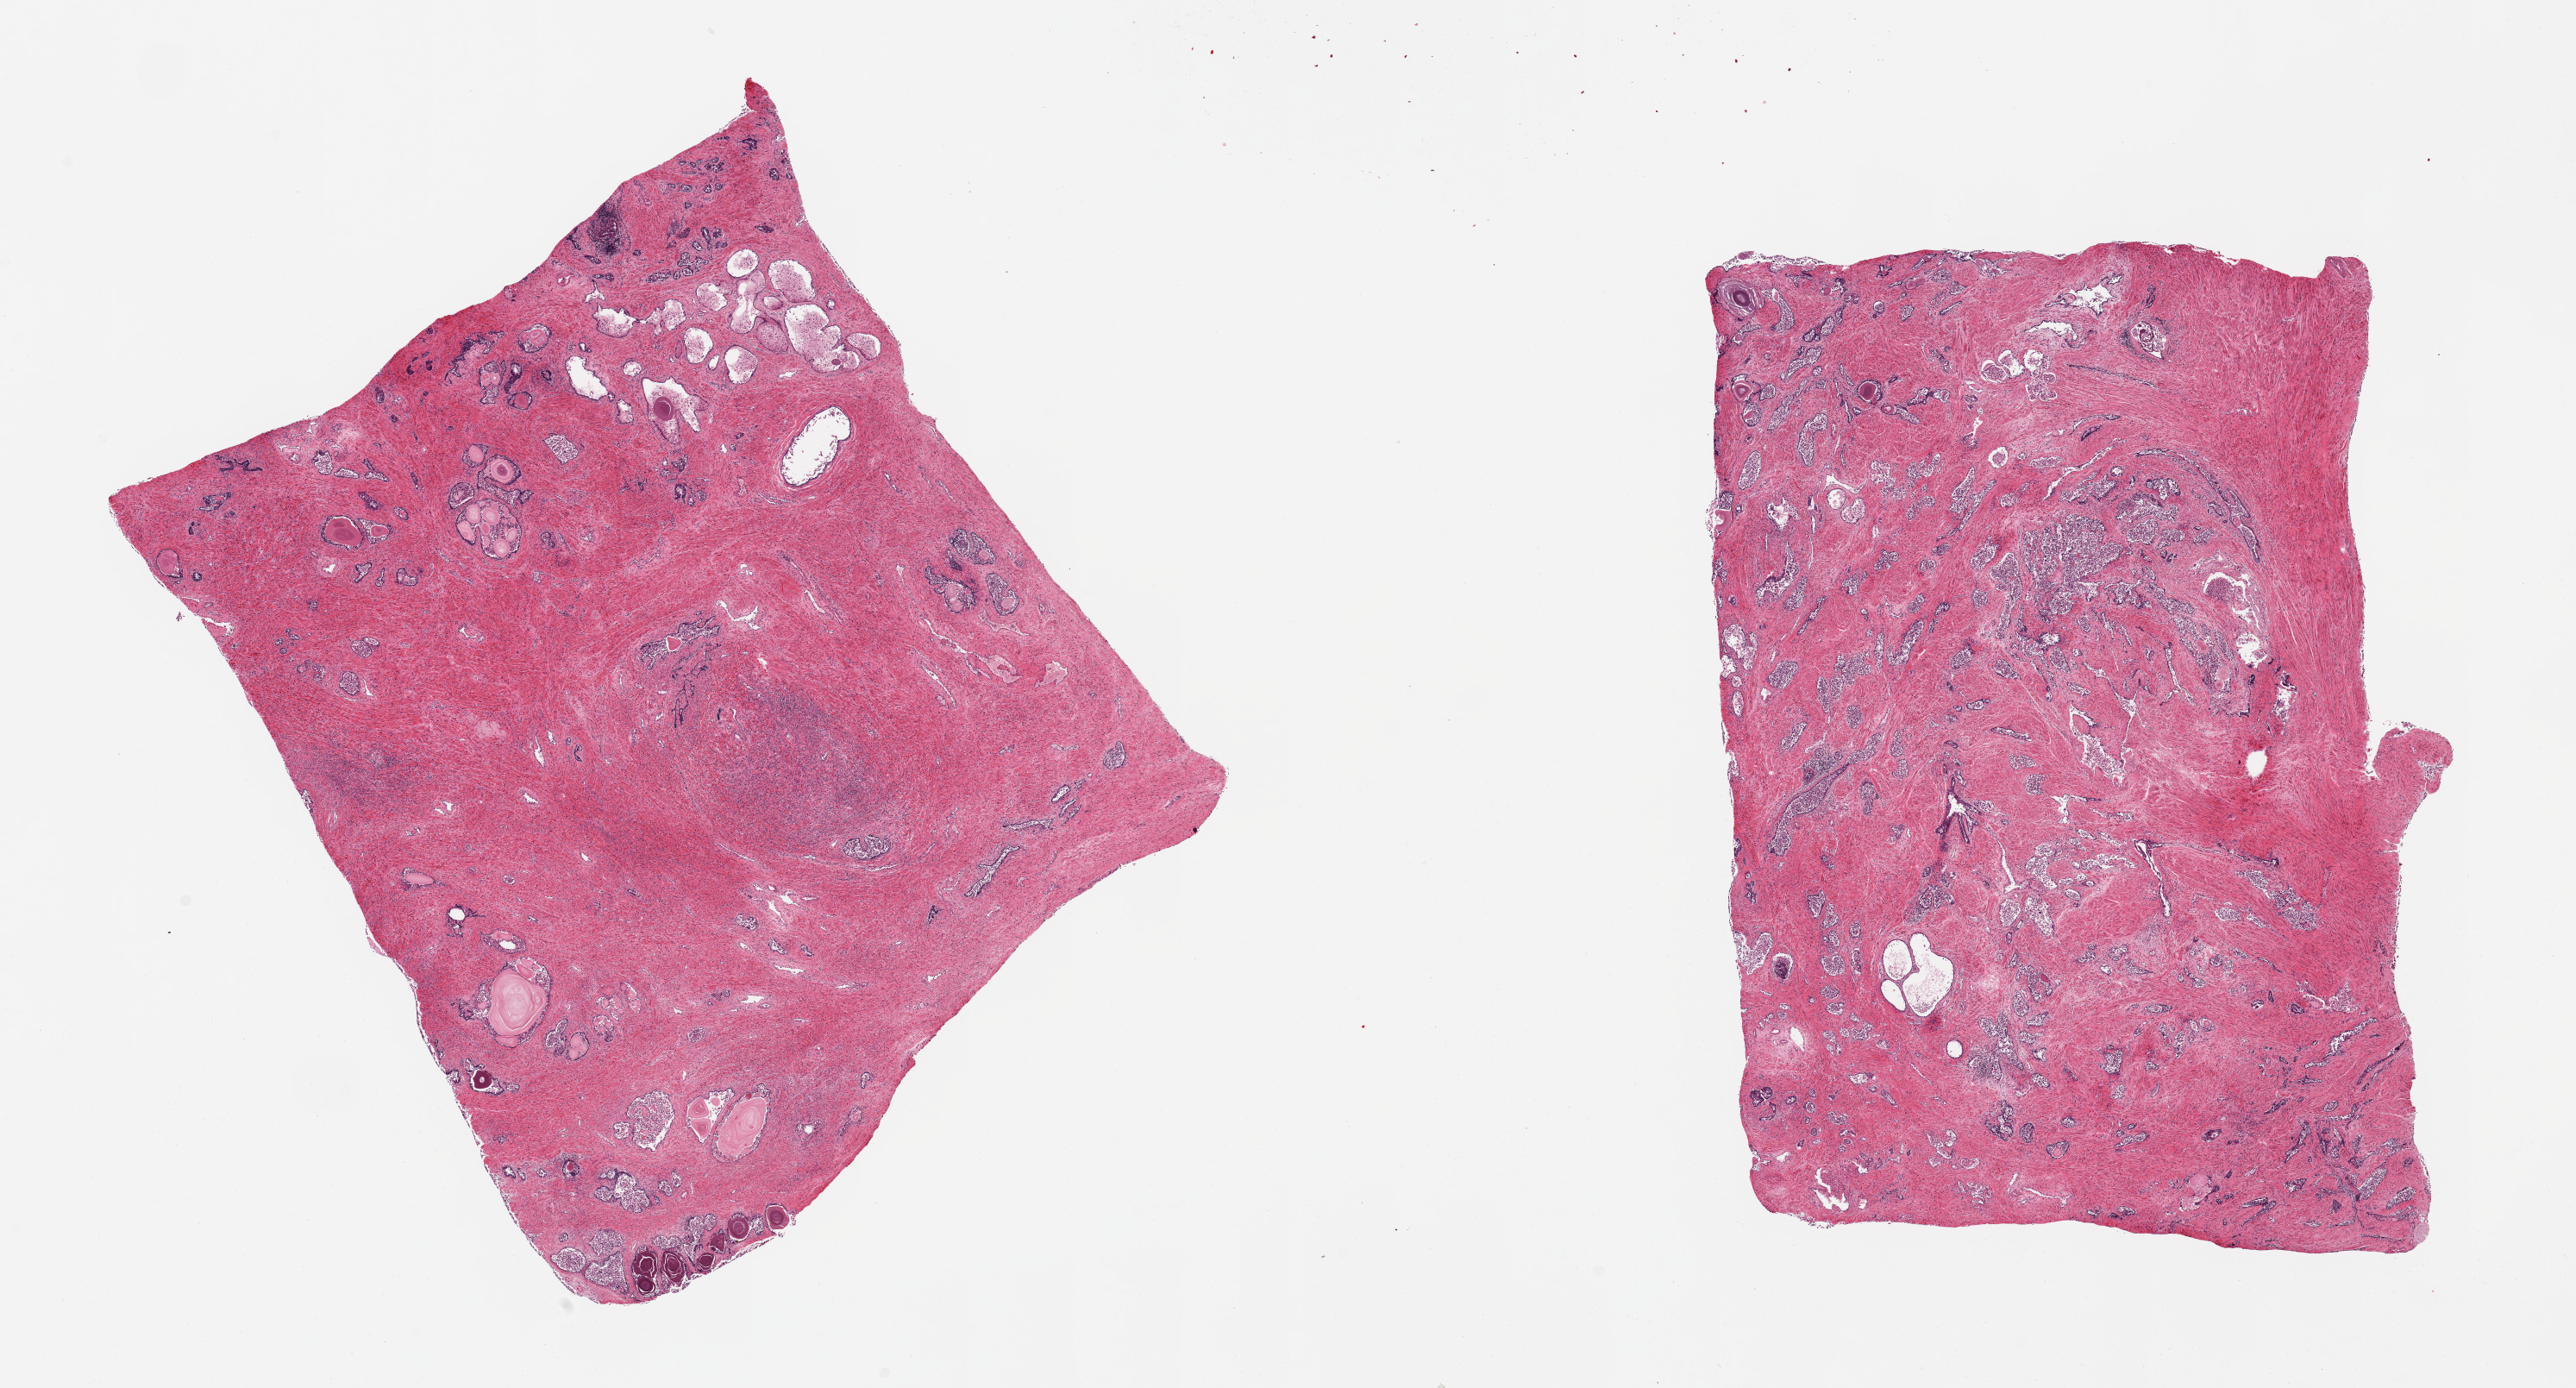
H&E whole-slide image, brightfield, shown as a low-resolution overview of the whole scanned area (about 23.6 x 12.7 mm). PAXgene-fixed paraffin-embedded (PFPE) section. Sampled site (target tissue): prostate. Tissue donor sample. Donor sex: male.
* pathologist's review note for this sample: 2 pieces, glandular elements markedly autolyzed